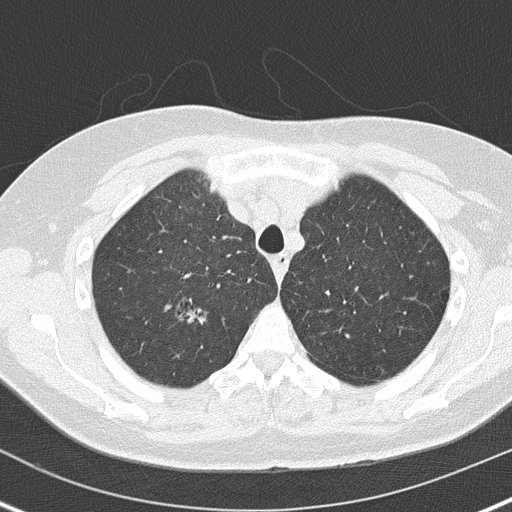
Low-dose screening chest CT, axial slice, first (baseline) screen, lung window (W 1500 / L -600 HU), lung (sharp) reconstruction kernel (B50f), slice 35 of 162 in the series, 512 × 512 image matrix. Female participant, aged 61 years at enrolment. Current smoker at enrolment.
Expert-annotated lung lesion, box from (x=181, y=298) to (x=219, y=331) px. Reader record for this screening exam (exam-level; its link to the box is not recorded): non-calcified nodule or mass ≥4 mm, right upper lobe, 8 × 5 mm, smooth margins, soft tissue attenuation. Official screen result: positive, change unspecified: nodule(s) >= 4 mm or enlarging nodule(s), mass(es), or other non-specific abnormalities suspicious for lung cancer. Later outcome: lung cancer diagnosed 438 days after this screen — adenocarcinoma, NOS, right upper lobe, moderately differentiated (G2), stage IA (AJCC 6th edition), 20 mm at pathology.